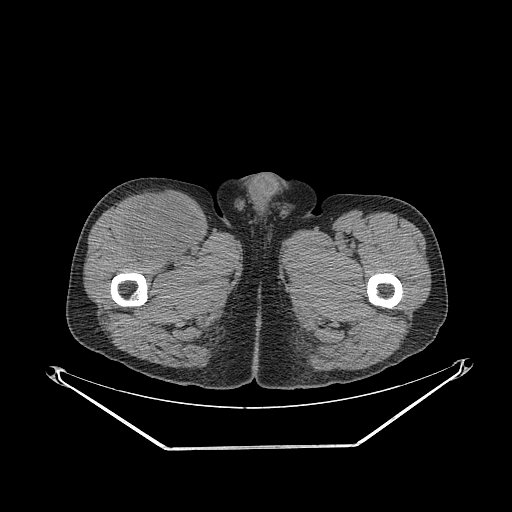
CT of an extremity soft-tissue mass (from a PET/CT study), one axial slice. Slice 297 of 311 in the series (ordered by position). Soft-tissue window (W 400 / L 40 HU). 512 × 512 image matrix, field of view 500 × 500 mm. Male patient. From the clinical record (not read from this slice): histological type: pleiomorphic leiomyosarcoma; grade: intermediate; site of the primary tumour: right thigh.
Annotated regions visible in this slice (expert contour drawn on MRI and transferred to this co-registered scan by the dataset authors):
- gross tumour volume including surrounding oedema: box from (x=123, y=194) to (x=202, y=261) px
- gross tumour volume (mass): (x=123, y=194)–(x=202, y=261)